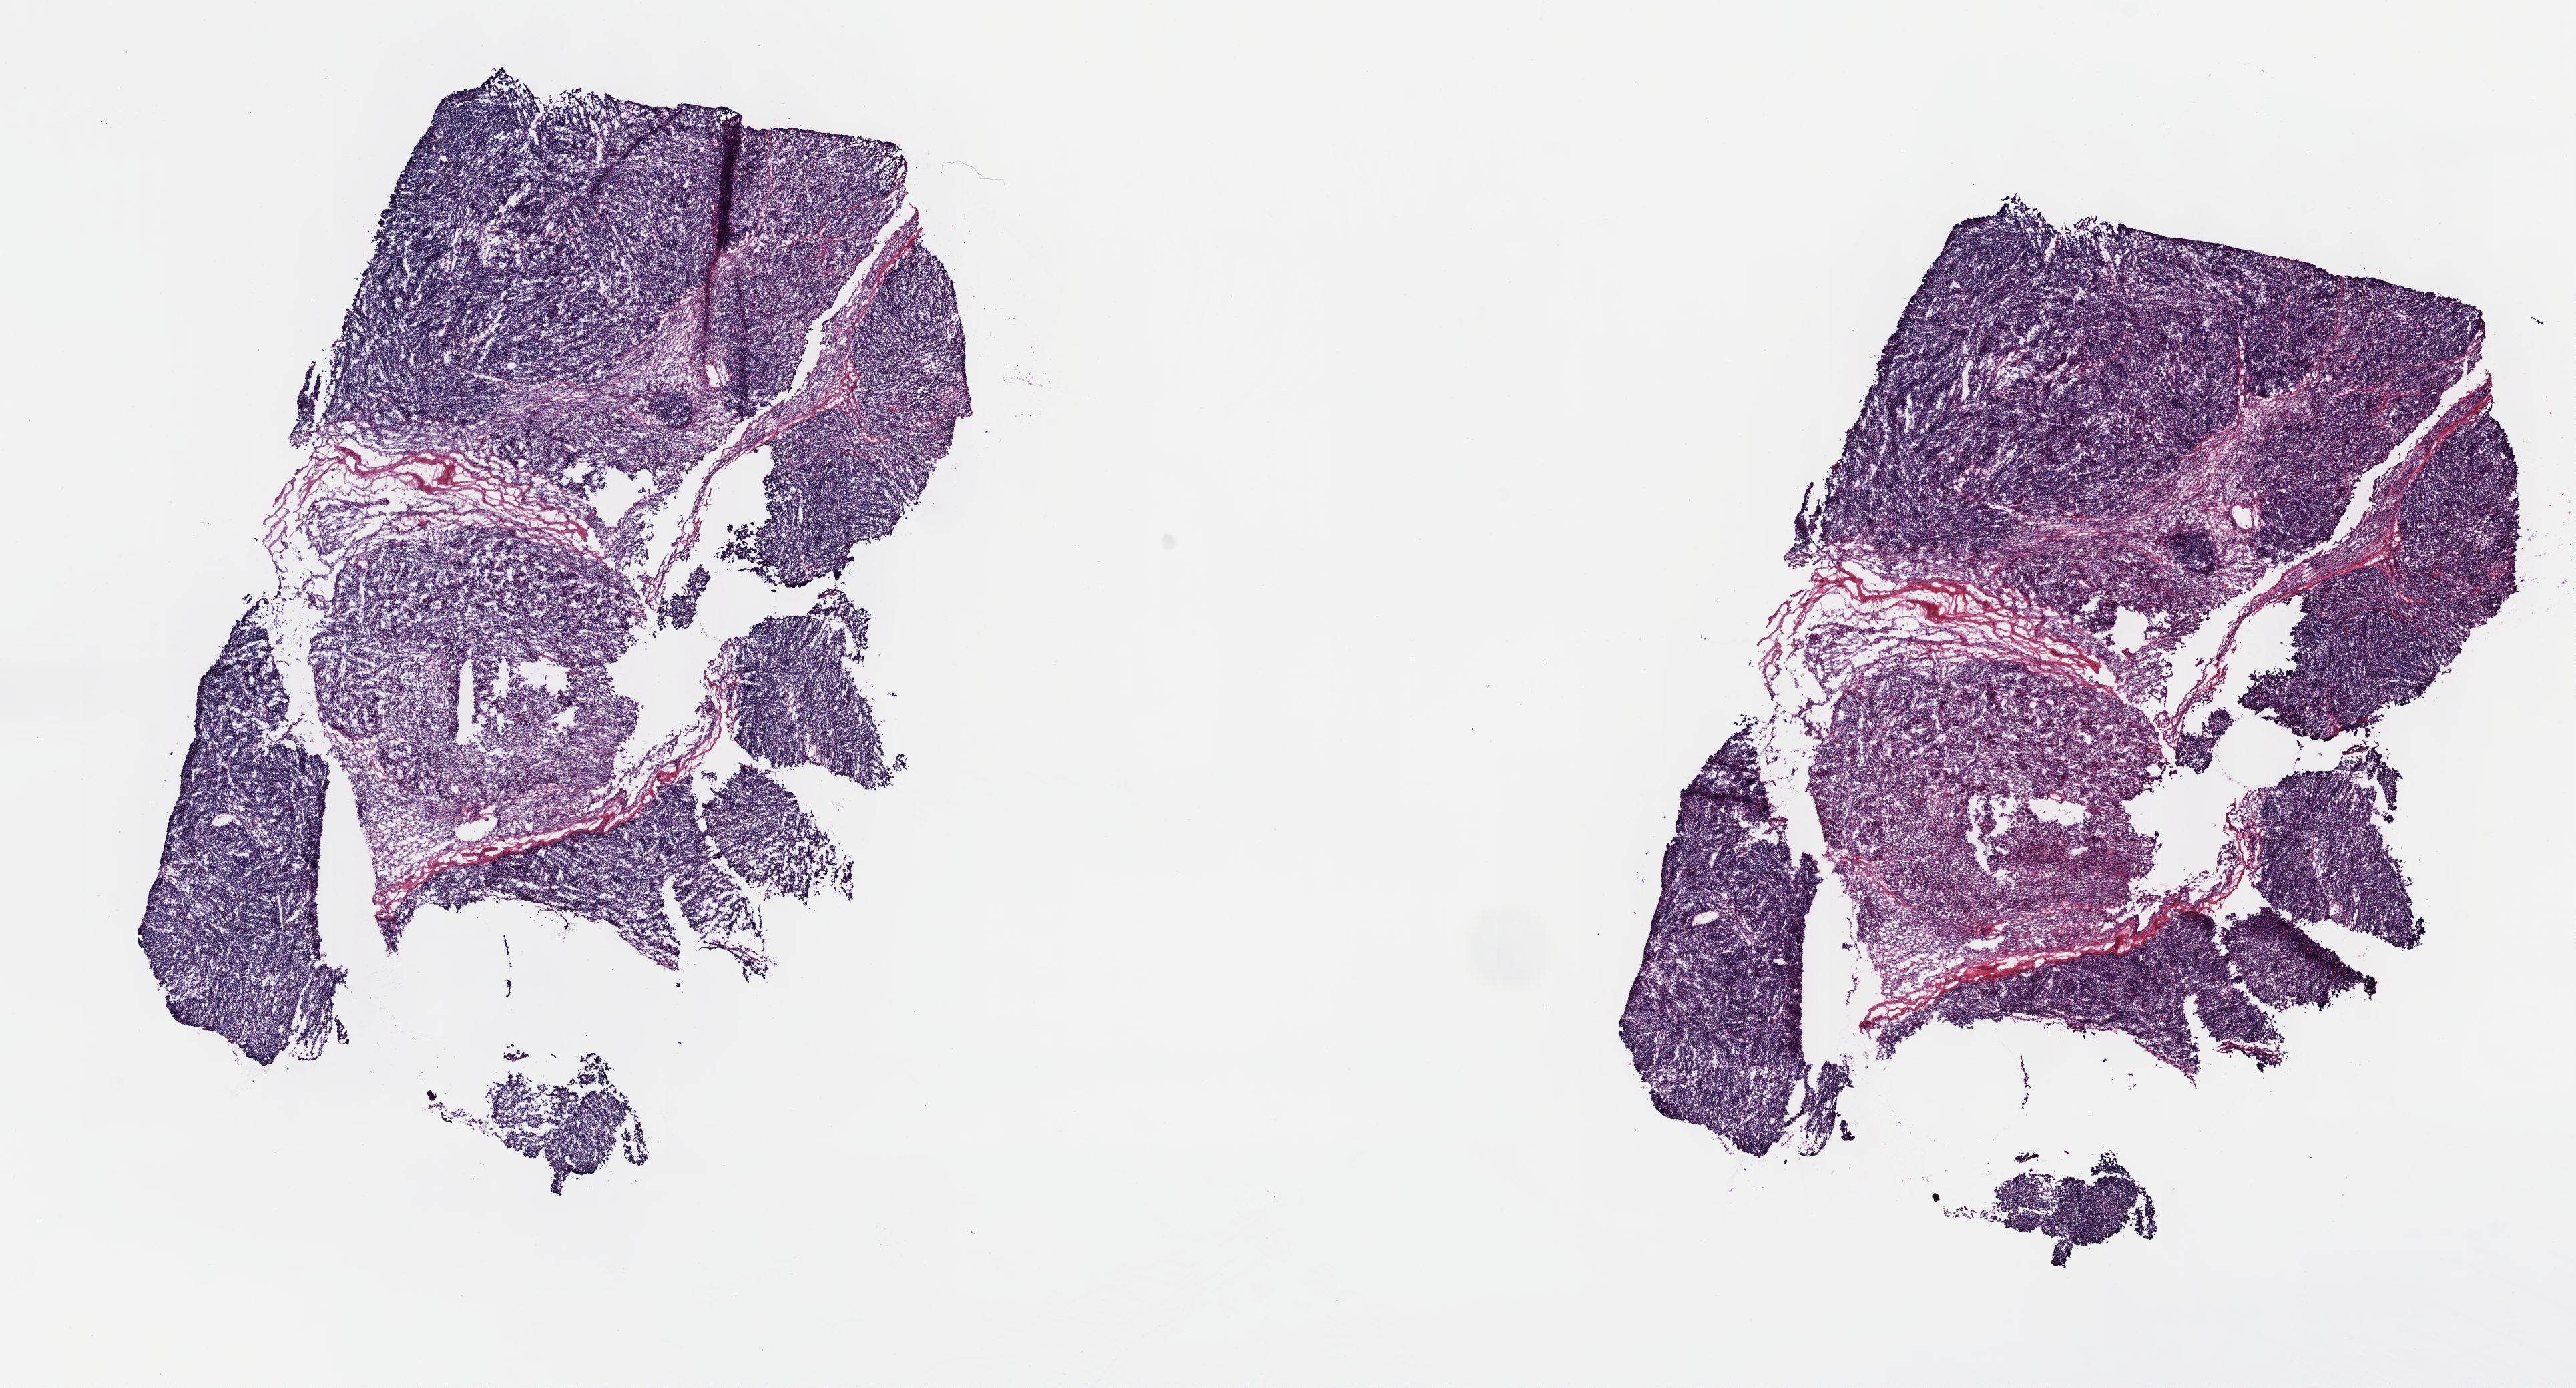
H&E-stained whole-slide image, shown as a low-resolution overview of the whole scanned area (about 15.6 x 8.4 mm, acquisition: 40x scan). Frozen section from the top of the tissue portion. Sample: primary tumour, thymus. Female patient; age at initial diagnosis 55 years. Pathologist review of this section (percent, as recorded): tumour cells 100%, tumour nuclei 80%.
Pathologic diagnosis: Thymoma, type AB, NOS (anterior mediastinum).